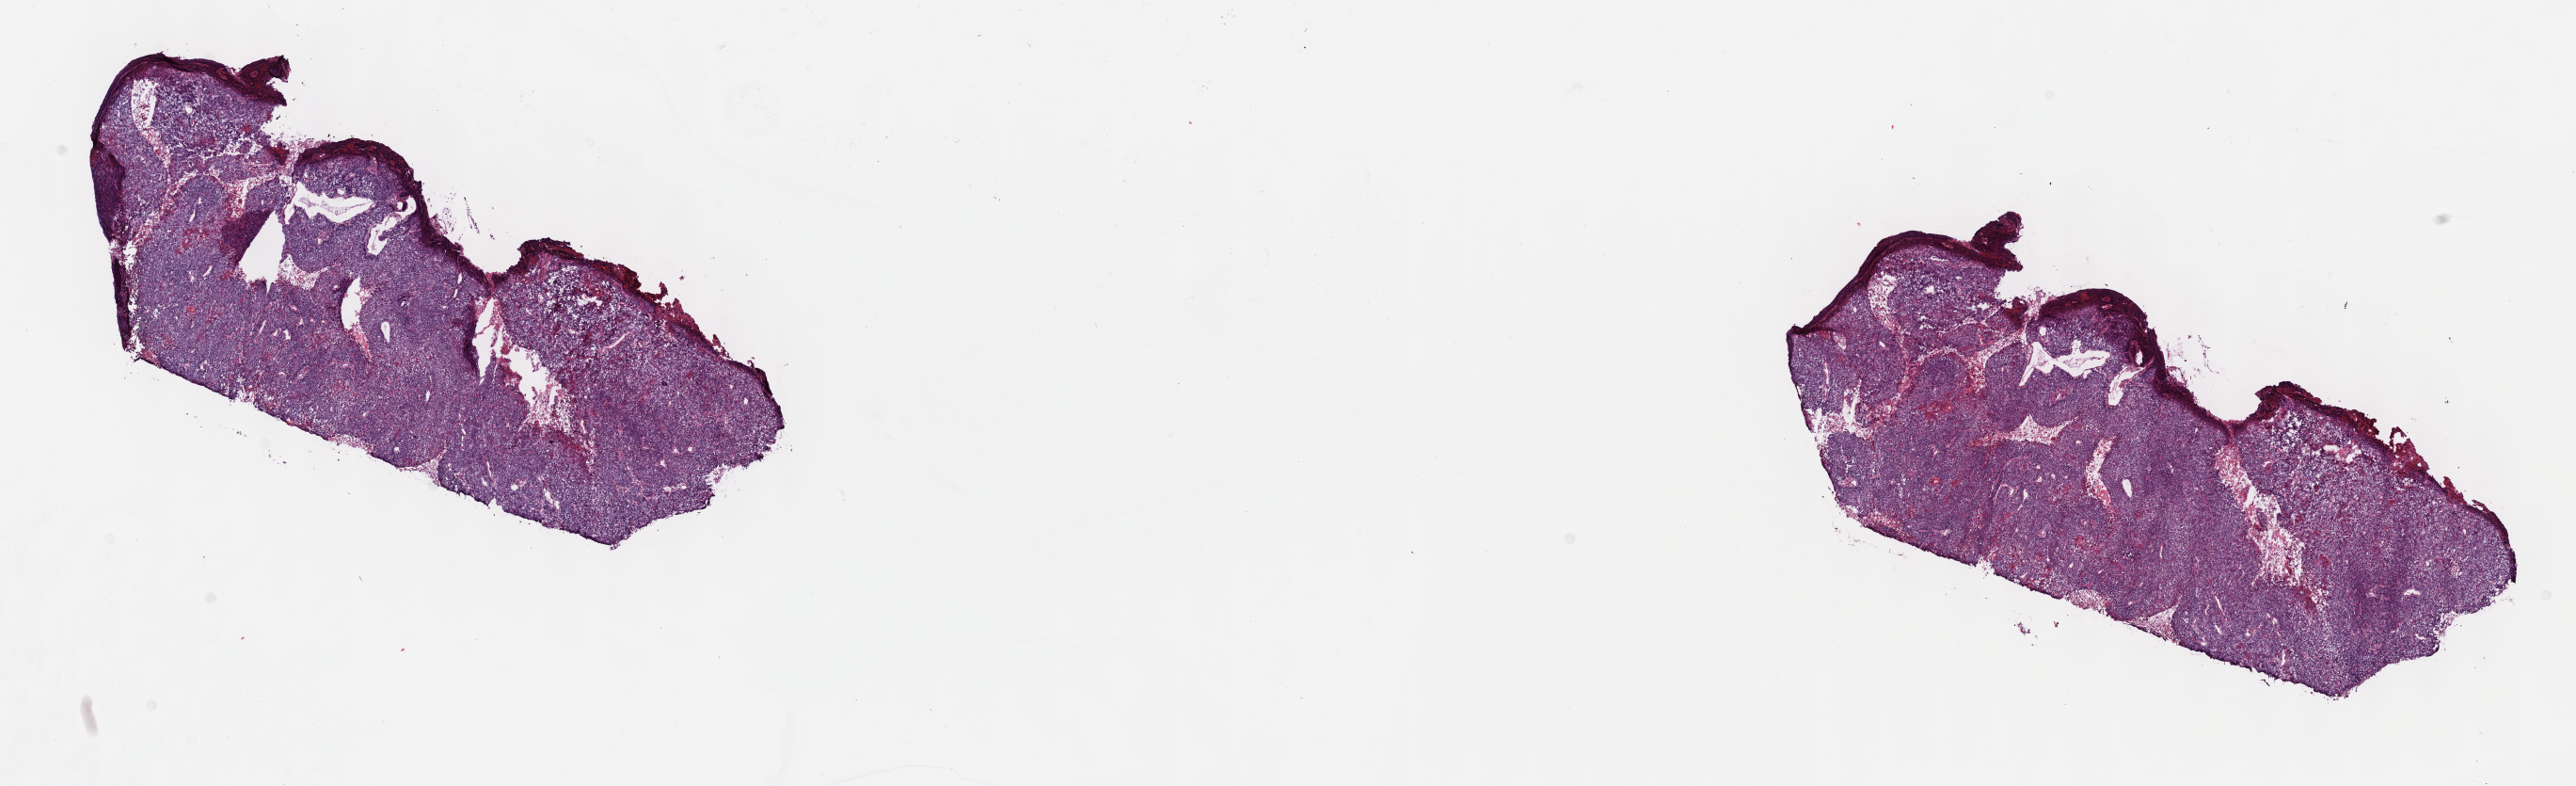
Whole-slide histology image, Hematoxylin and eosin (H&E) stained, shown as a low-resolution overview of the whole scanned area (about 22.1 x 6.8 mm, slide scanned at 40x); frozen section from the top of the tissue portion; cervix, primary tumour sample. Female patient; age at initial diagnosis 63 years. Histologic grade: GX (grade cannot be assessed). Pathologist review of this section (percent, as recorded): tumour cells 80%, tumour nuclei 80%, normal cells 0%, stromal cells 10%, necrosis 10%. Inflammatory infiltration, as recorded: lymphocyte infiltration 40%, monocyte infiltration 20%, neutrophil infiltration 20%.
Pathologic diagnosis: Squamous cell carcinoma, NOS (cervix uteri). FIGO stage: IVA.